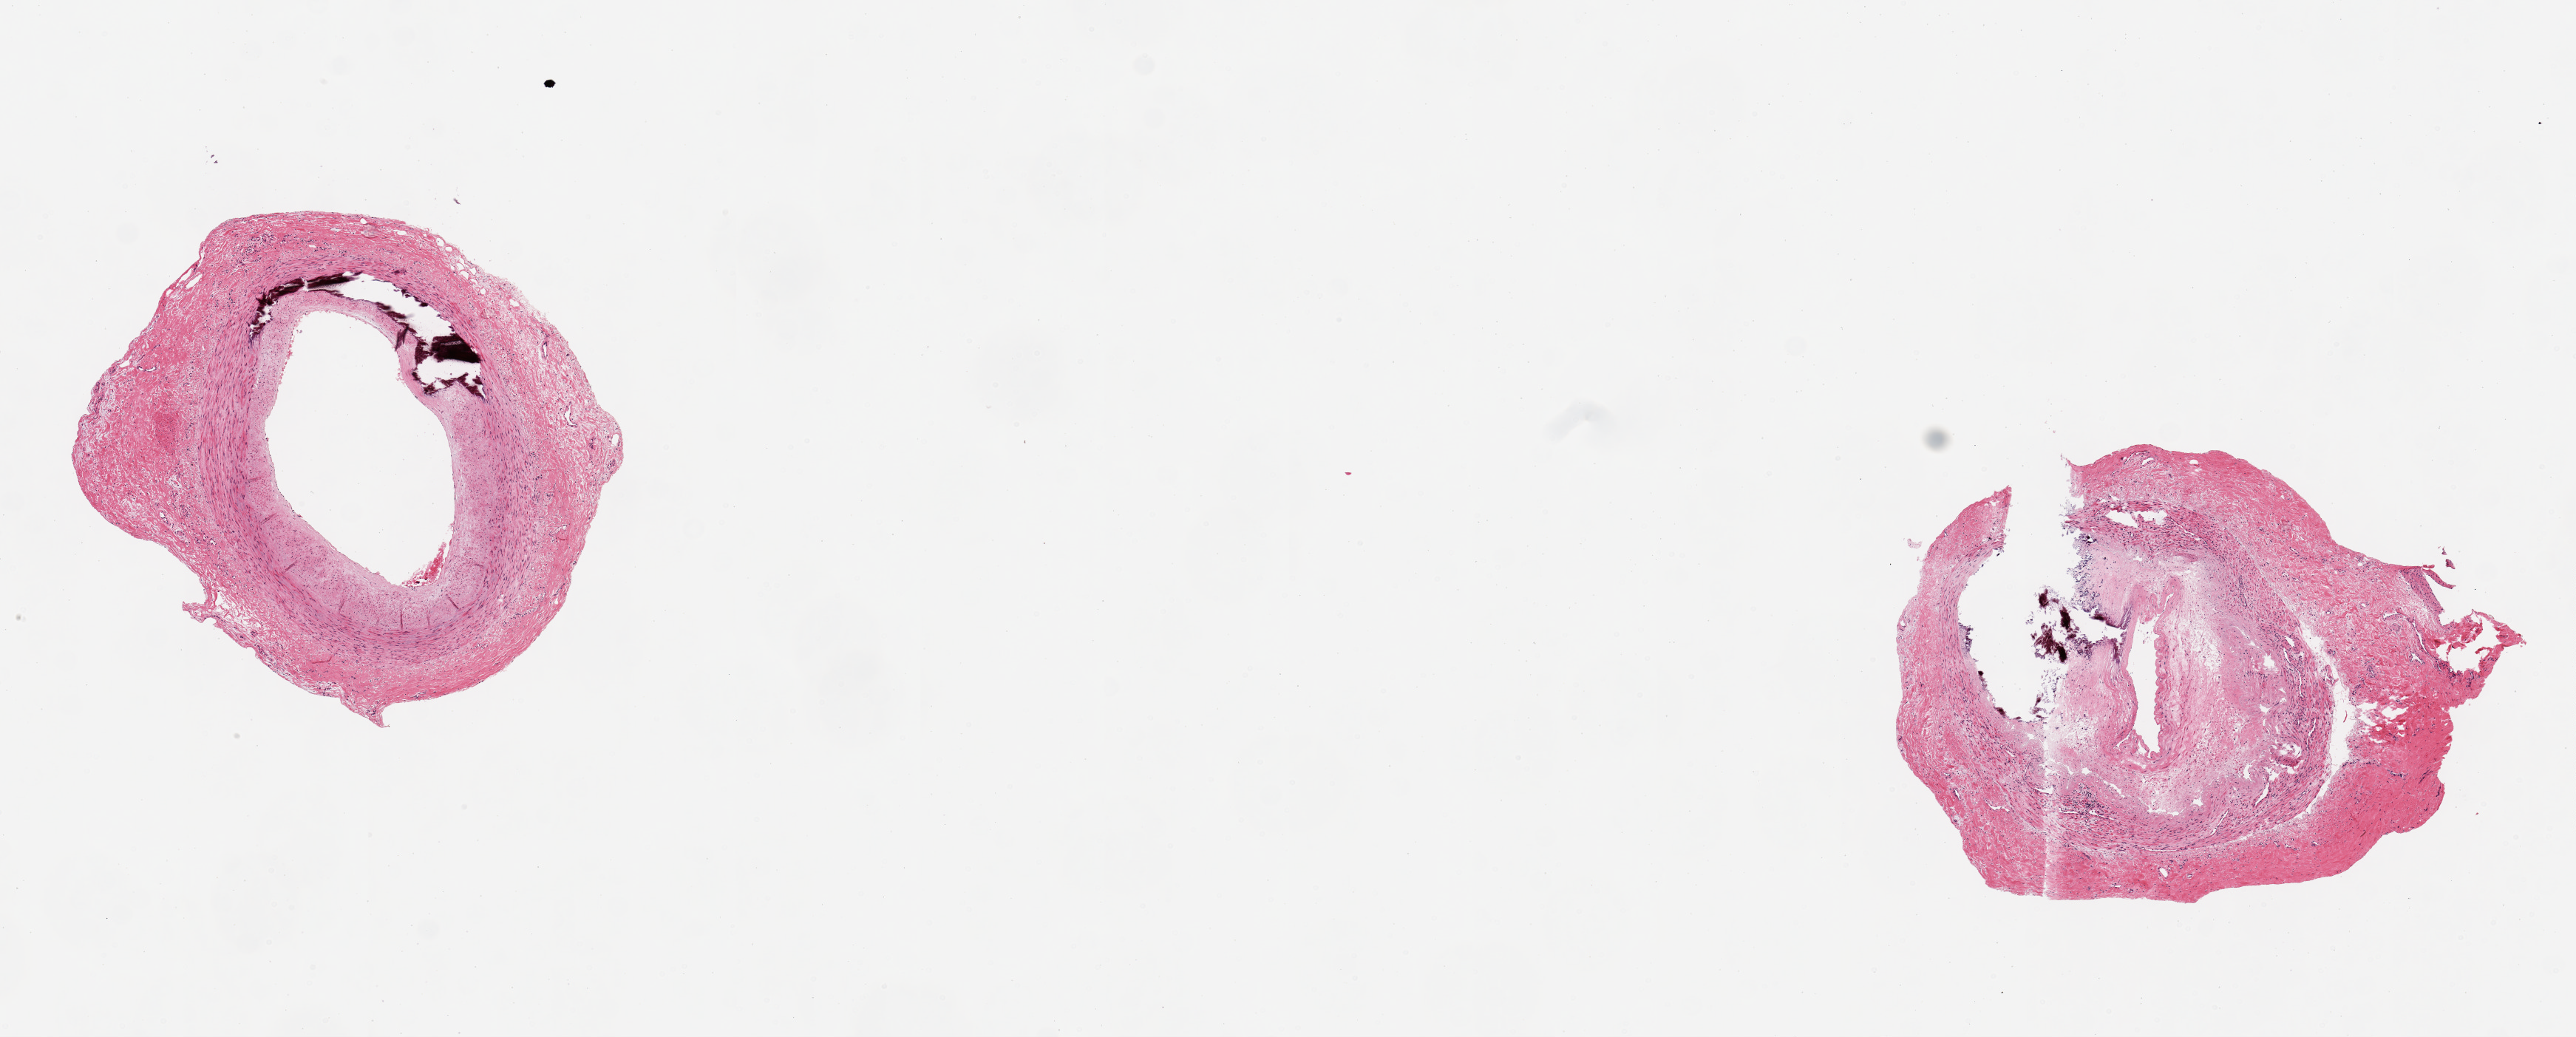
Digitized H&E-stained section, a low-resolution overview of the entire scanned area, about 13.8 x 5.5 mm; PAXgene-fixed, paraffin-embedded tissue; section of tibial artery (target tissue); donor tissue sample. Male donor.
Pathologist's review note for this sample: 2 pieces ~2.5mm d. Subtotally occlusive calcified atherosclerosis. Good clean specimens.